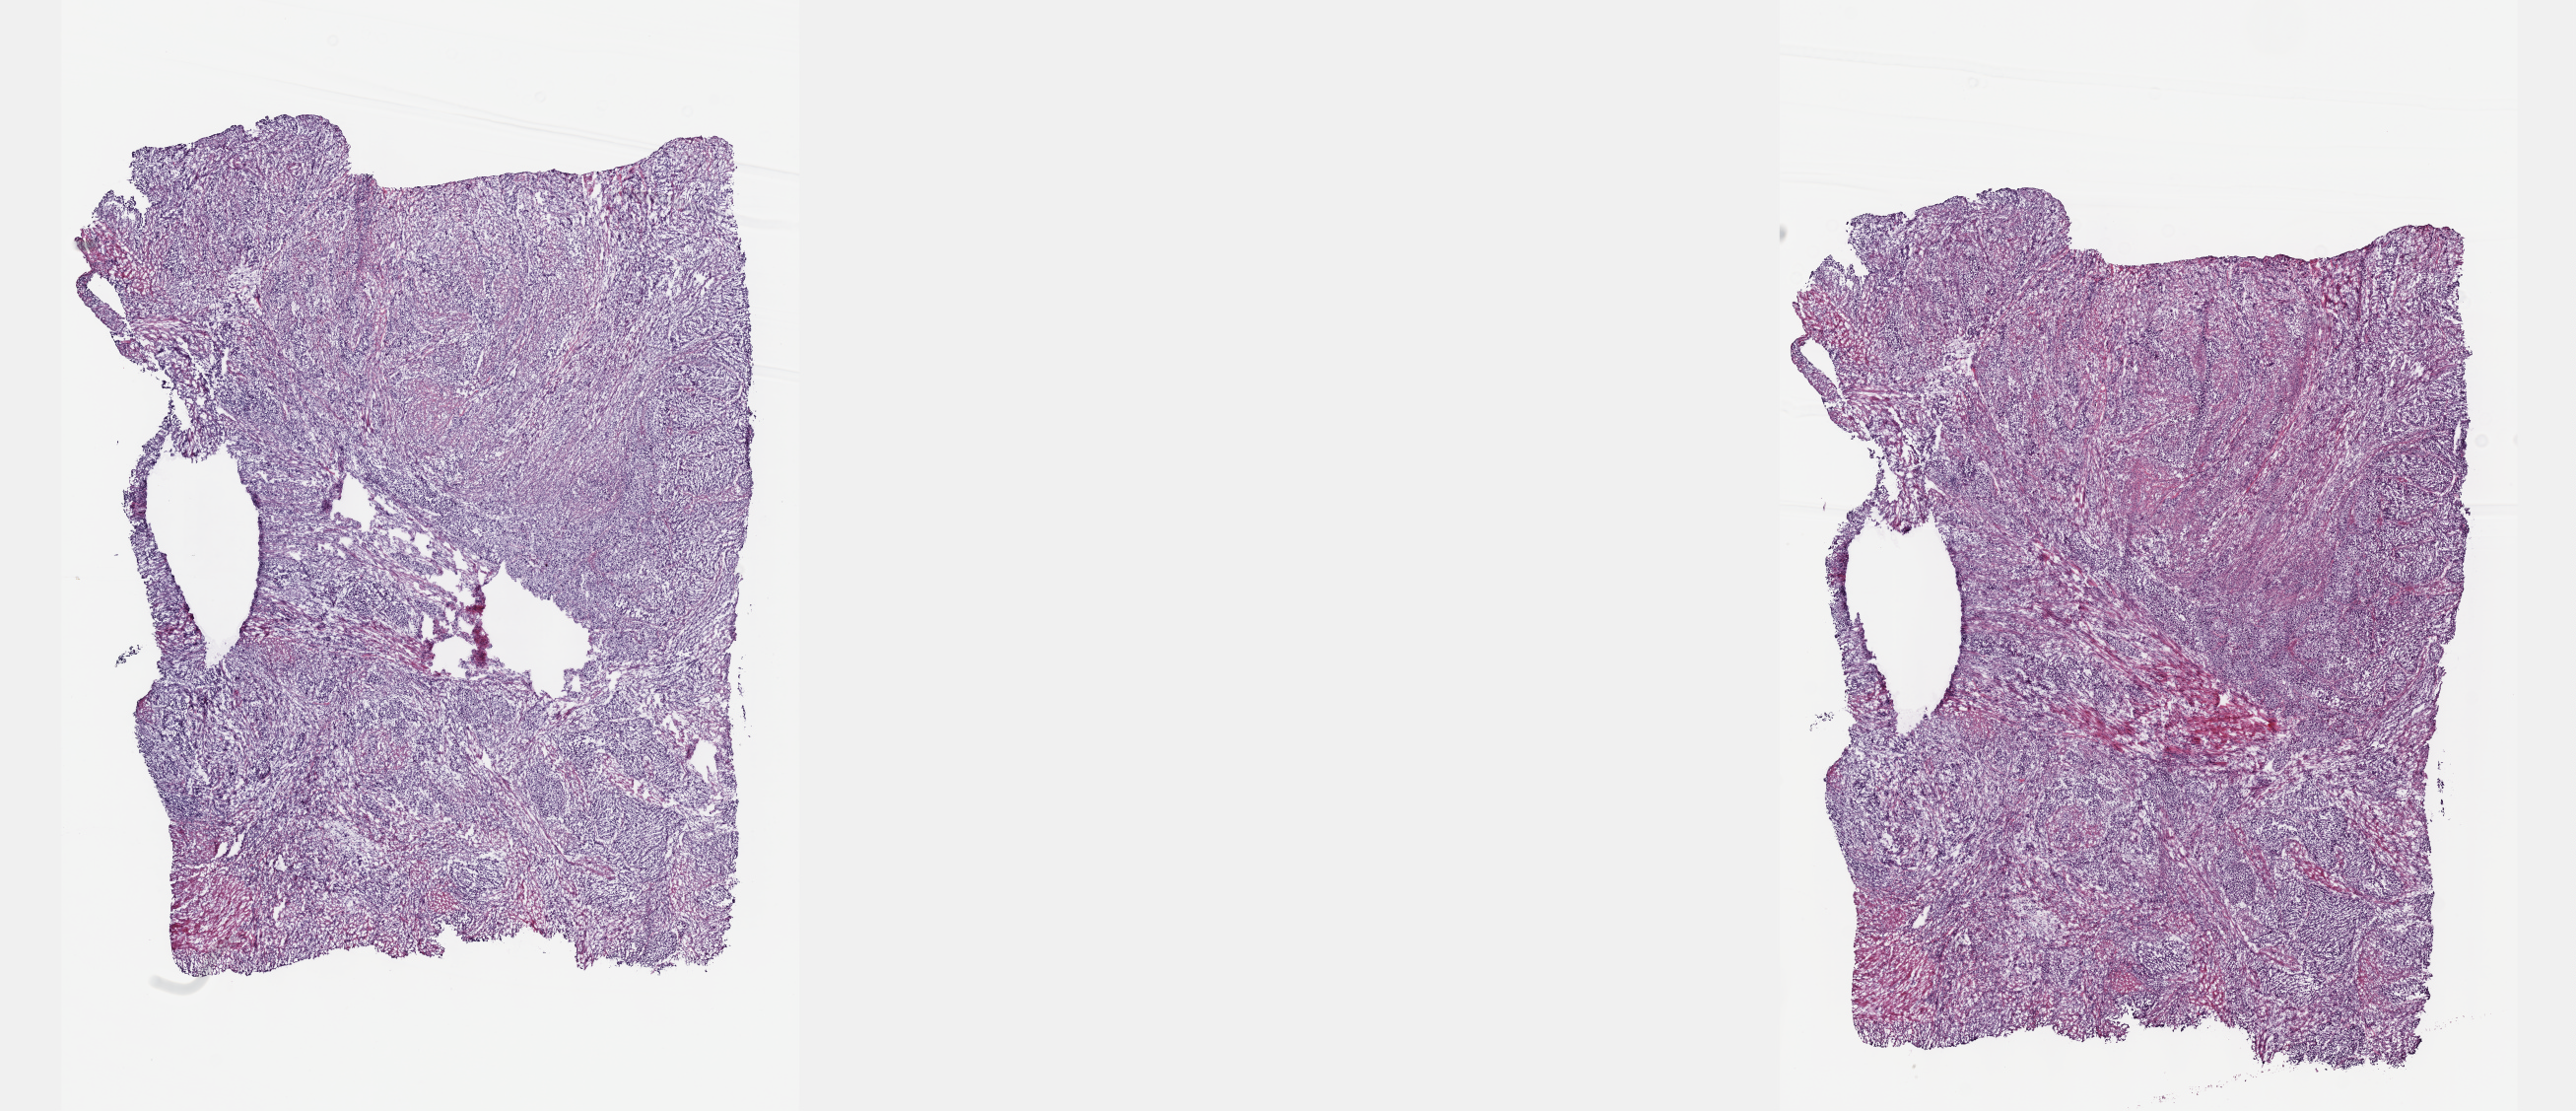
Whole-slide histology image, H&E — low-resolution overview of the scanned area, about 21.1 x 9.1 mm. Frozen section from the top of the tissue portion. Sample: primary tumour, bladder. Patient: male, age at initial diagnosis 70 years. Histologic grade: high grade. Slide review estimates, as recorded: tumour cells 80%, tumour nuclei 90%, normal cells 0%, stromal cells 20%, necrosis 0%. Inflammatory infiltration, as recorded: lymphocyte infiltration 0%, monocyte infiltration 0%, neutrophil infiltration 0%.
AJCC pathologic stage: III. Lymph nodes positive (case pathology): 0 of 44 examined. Diagnosis: Transitional cell carcinoma.